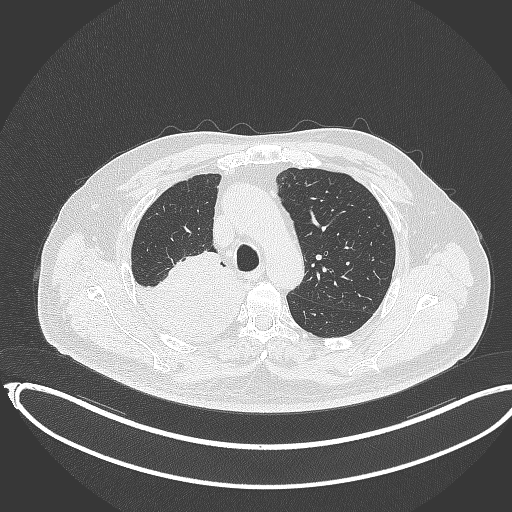
Chest CT, one axial slice; slice 264 of 403 in the series (ordered by position); 120 kVp; lung window (W 1500 / L -600 HU); 1 mm slice thickness; 512 × 512 image matrix. Male patient, age 68 years. Case-level facts recorded for this patient, not image findings: clinical TNM (as recorded): T2a N0 M0.
Outlined on this slice (bounding box drawn by a radiologist):
- lung tumour (recorded histology: adenocarcinoma): bounding box [x1, y1, x2, y2] px = [134, 254, 251, 345]